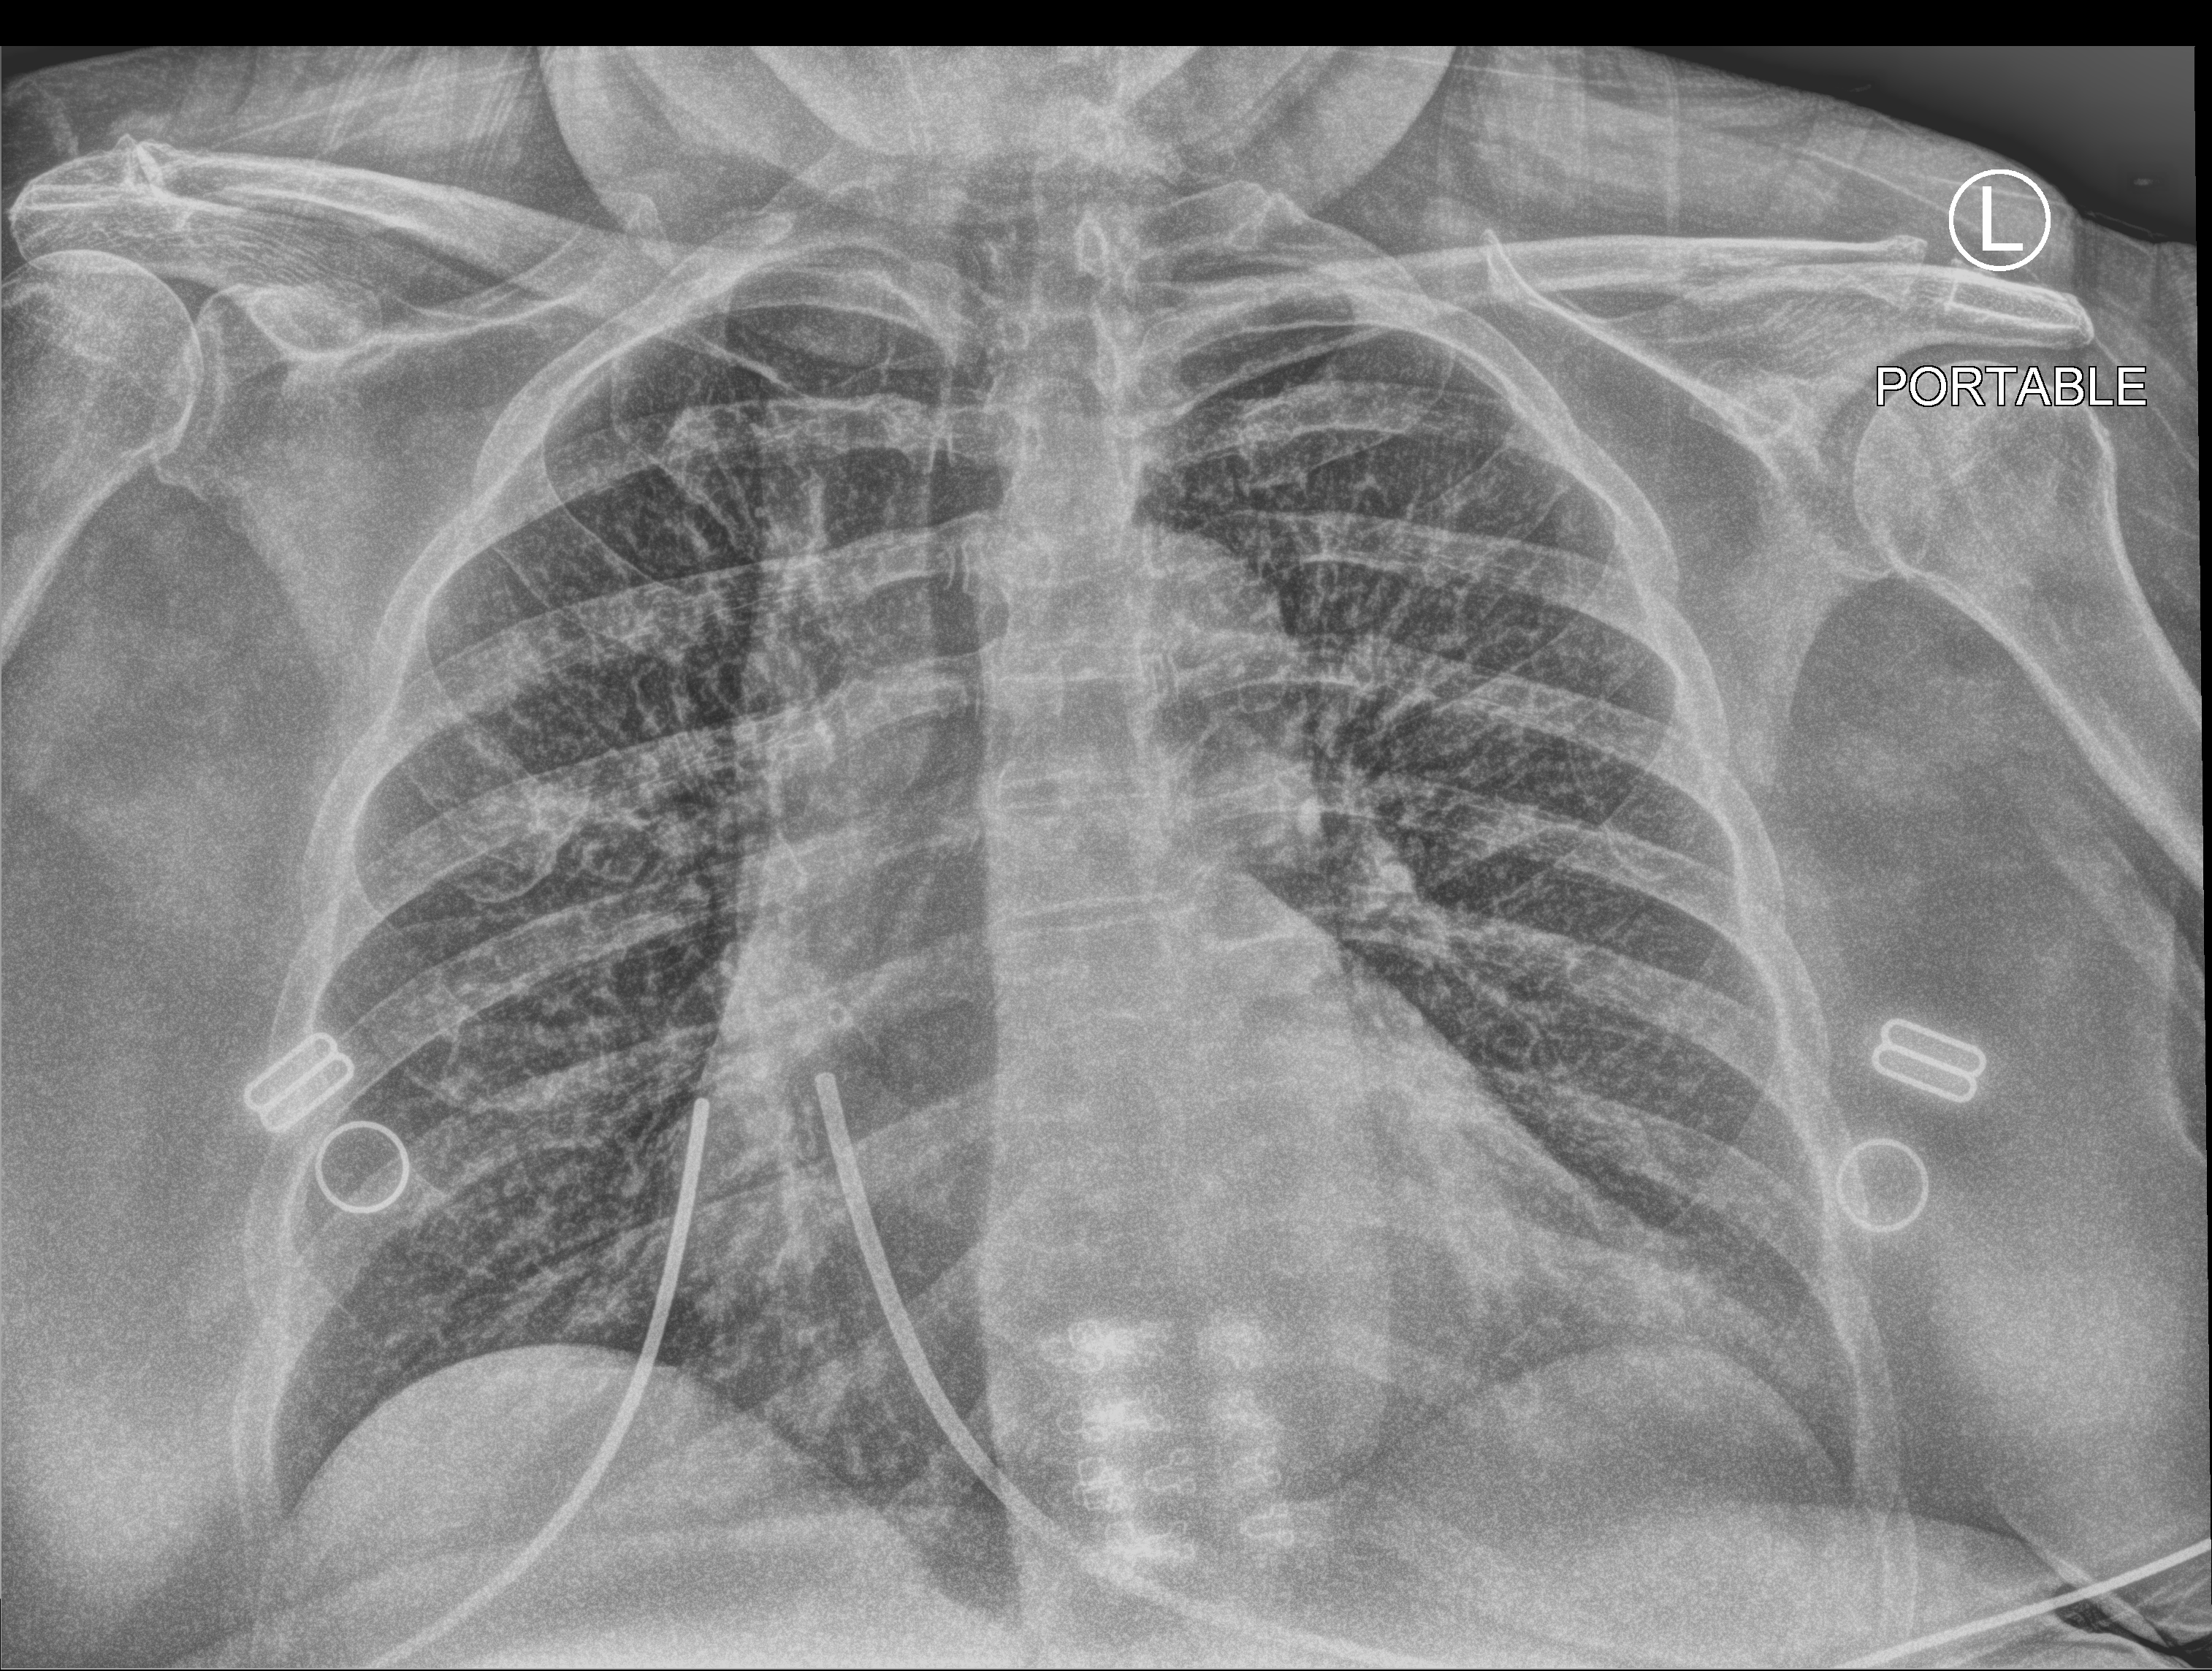
Chest X-ray (portable); anteroposterior (AP) projection. Female patient hospitalised with COVID-19, age 60–74 years.
Hospital-stay facts (about this admission, not read from this image; timing relative to this image not recorded): admitted to intensive care during this hospital stay: no; mechanically ventilated during this hospital stay: no; length of hospital stay: 2 days.